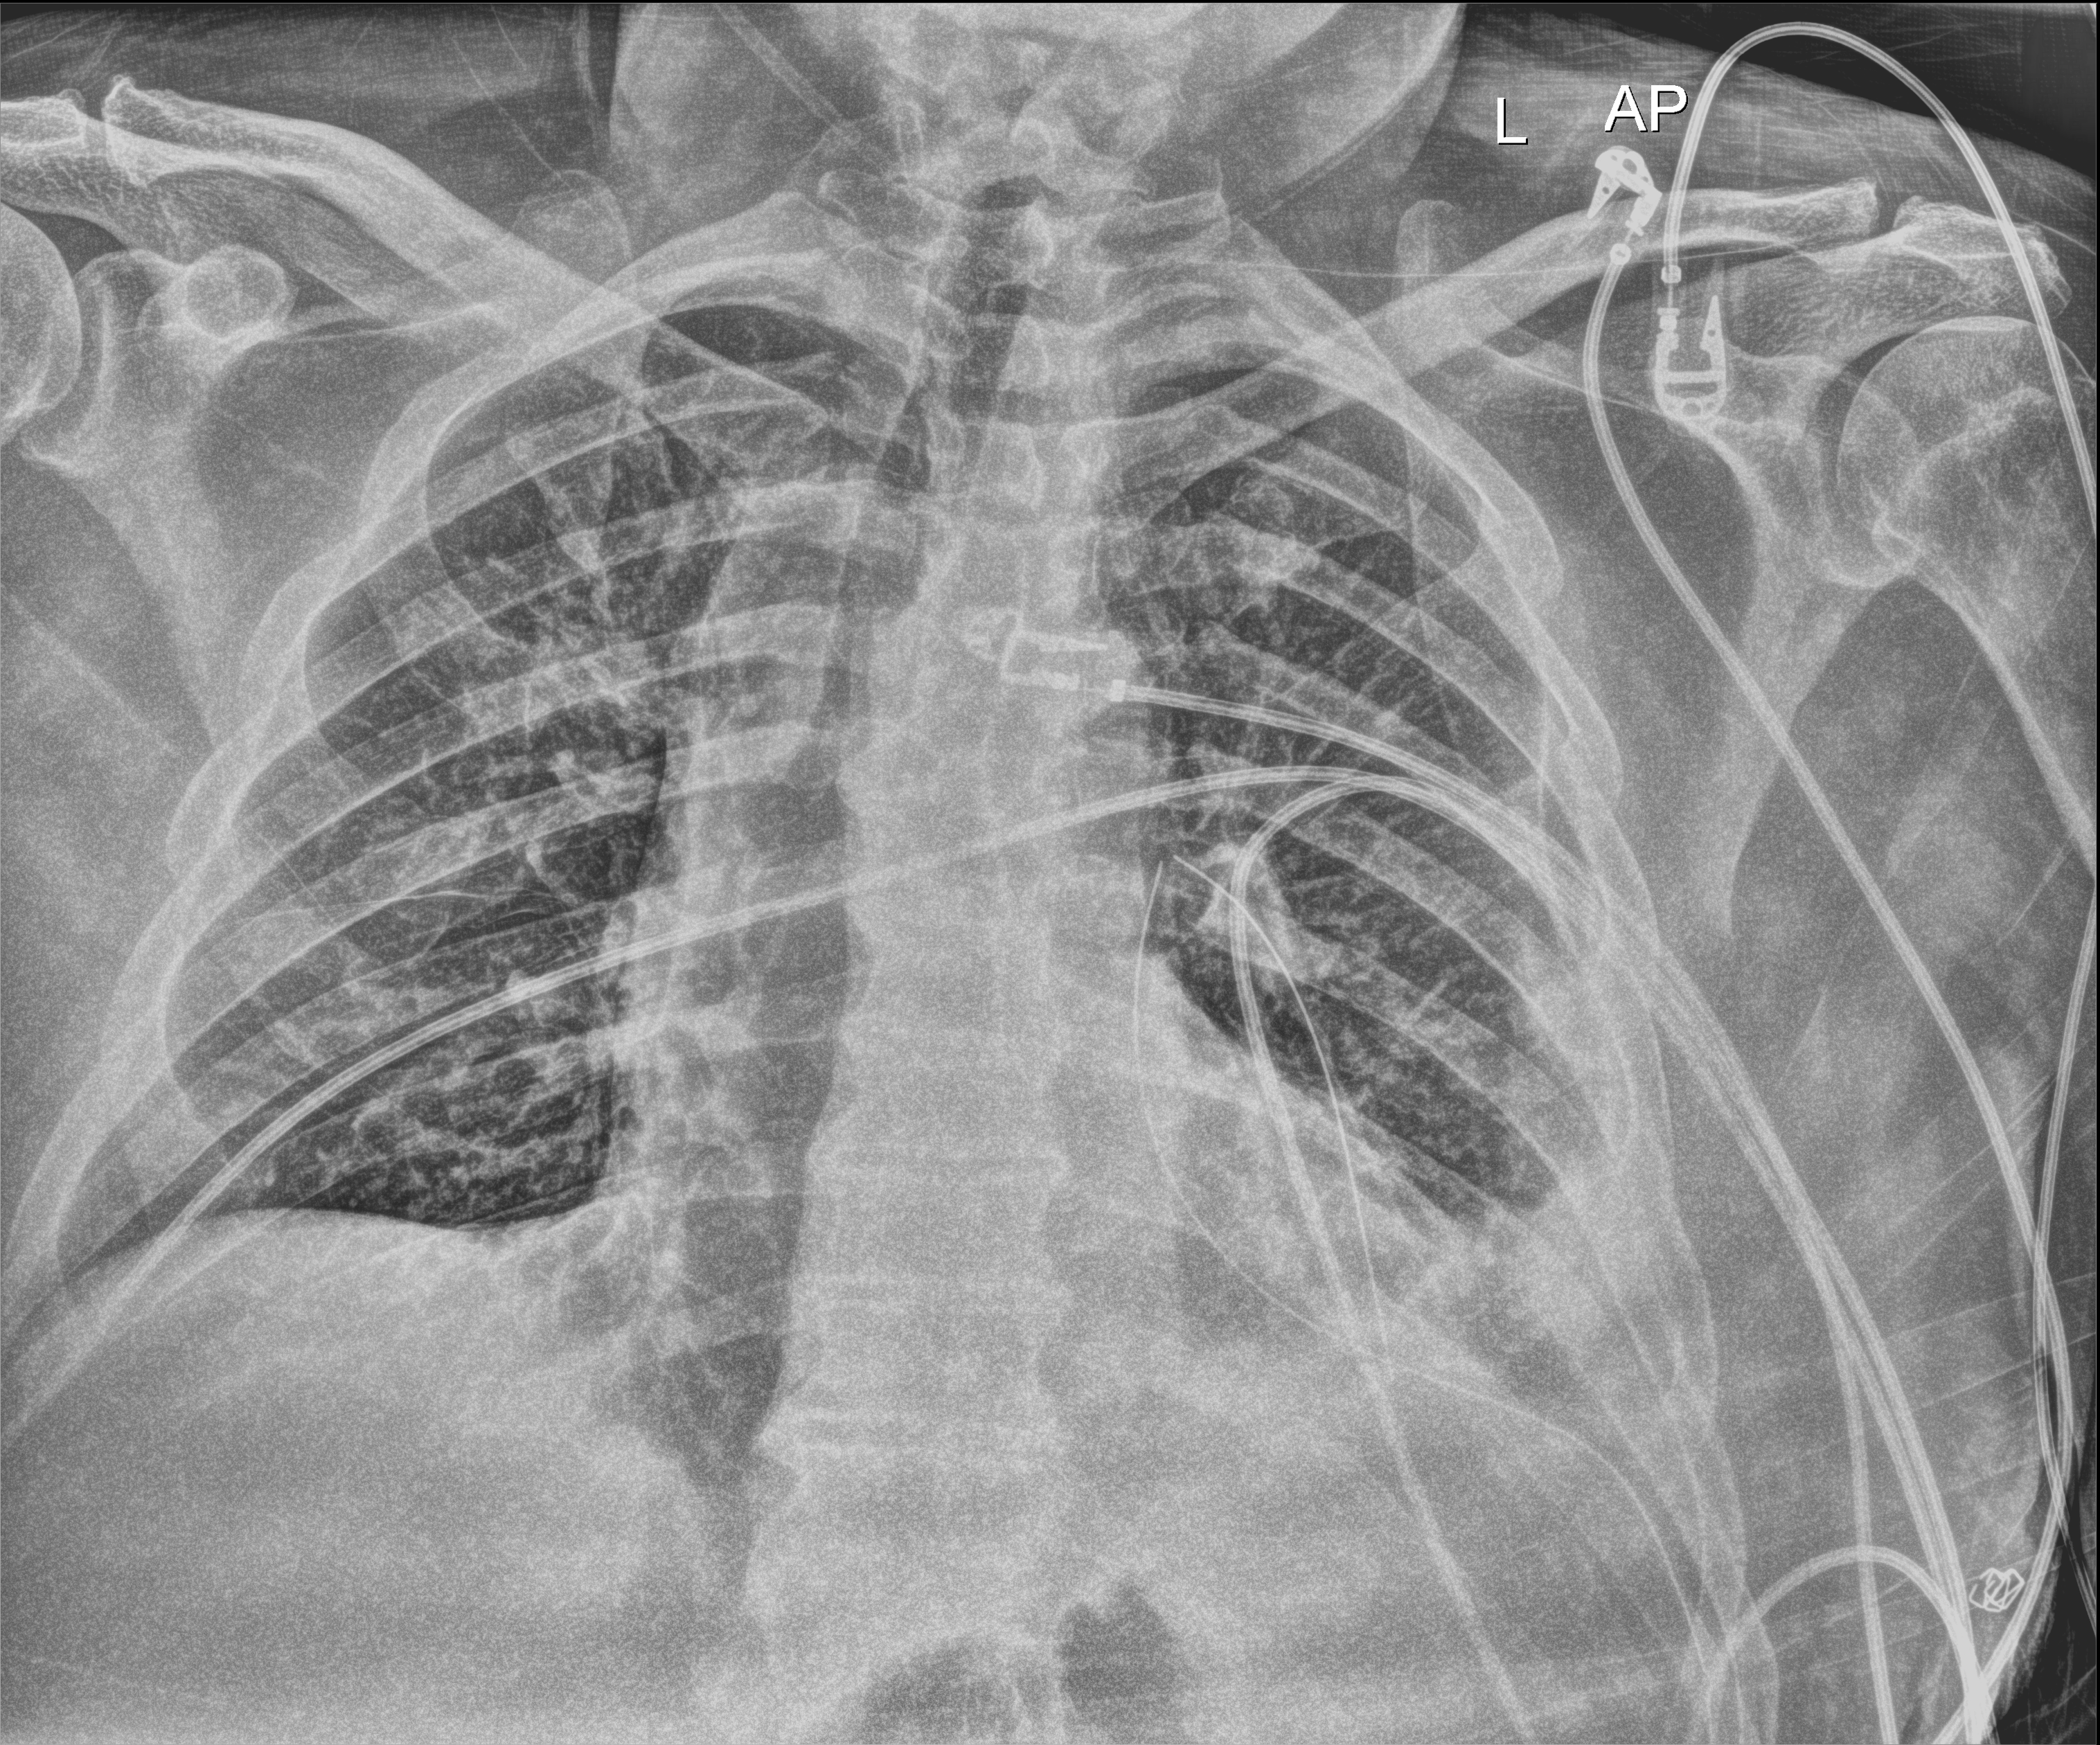
Bedside chest radiograph (digital radiography). Male patient hospitalised with COVID-19, age 18–59 years.
From the hospital-stay record, not from the radiograph (when in the stay this image was taken is not recorded): length of hospital stay: 10 days; admitted to intensive care during this hospital stay: no.